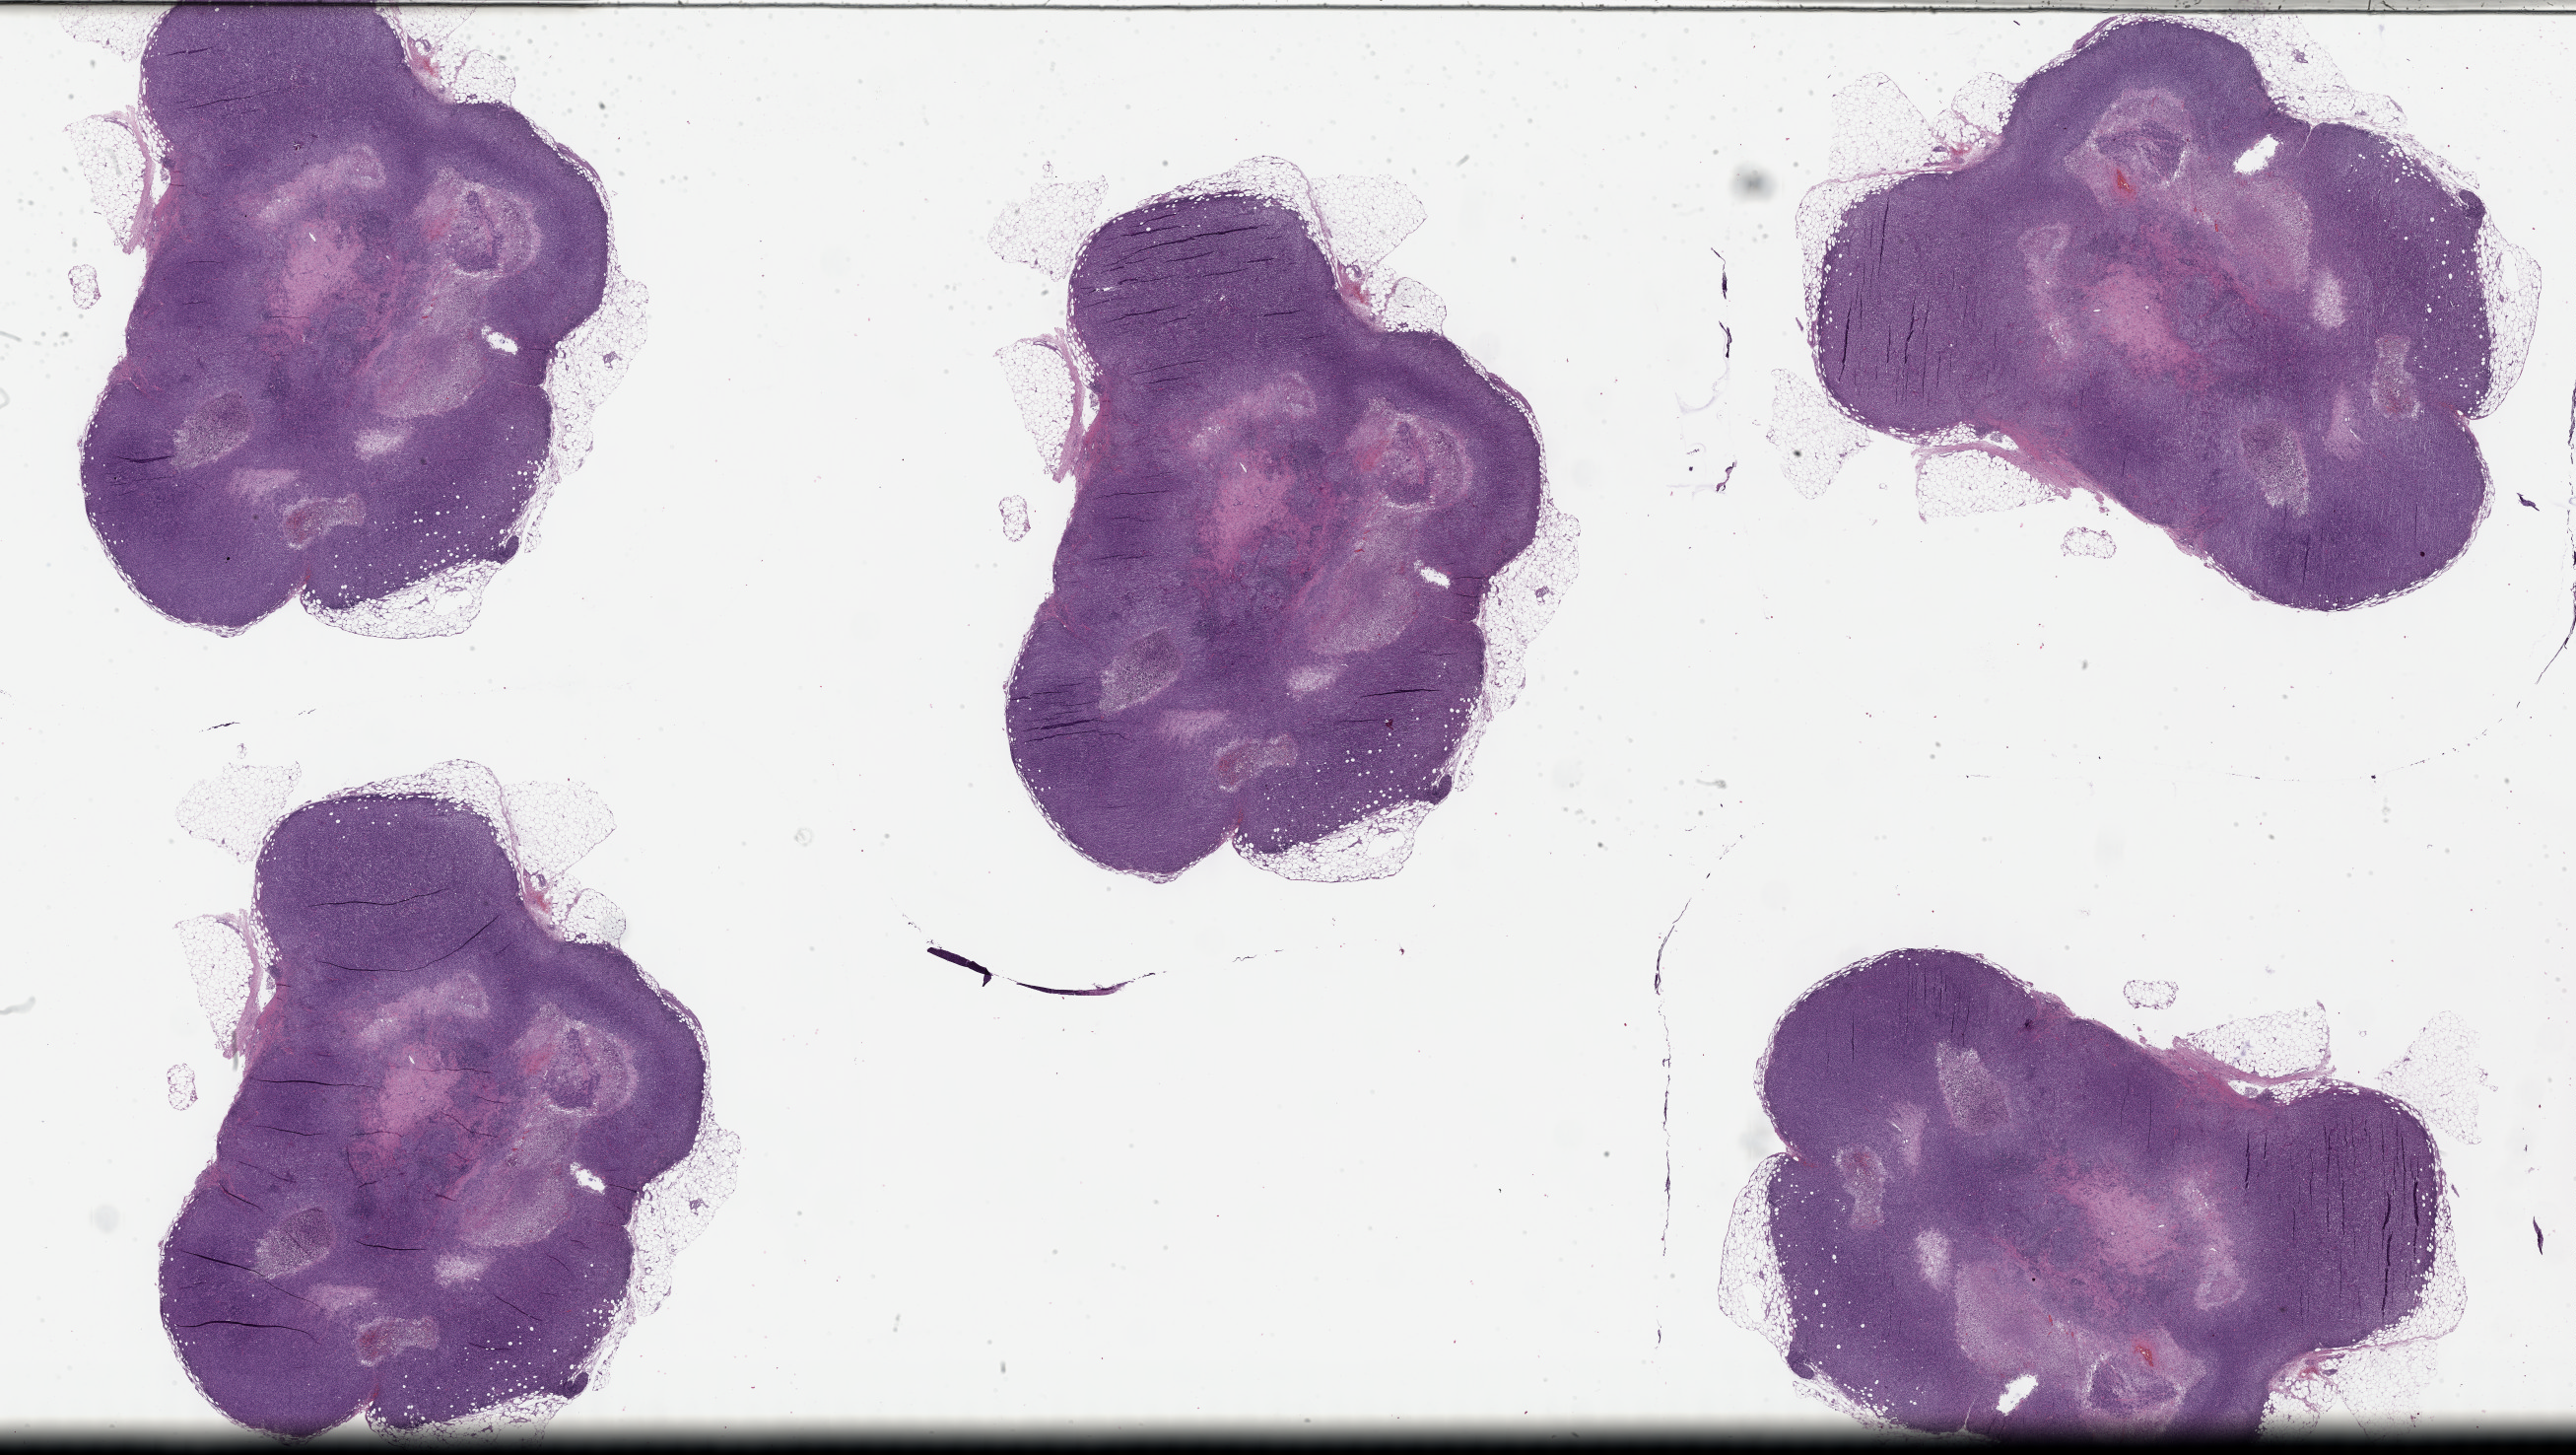
Whole-slide histology image, H&E-stained, a low-resolution overview of the entire scanned area, about 42.3 x 23.9 mm (from a 40x scan), formalin-fixed paraffin-embedded (FFPE) diagnostic section, sample: primary tumour, skin. Patient: female, age at initial diagnosis 42 years.
Histologic diagnosis: Malignant melanoma, NOS.